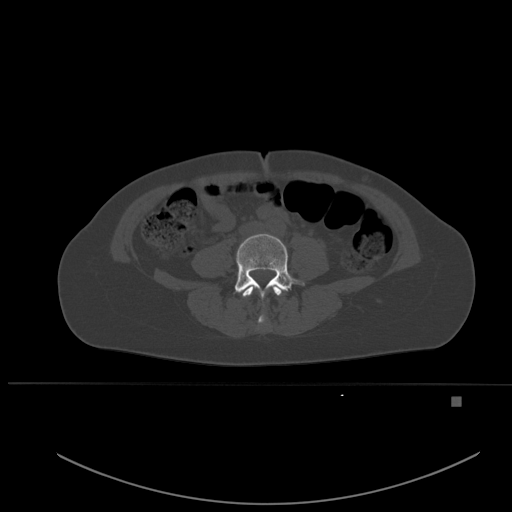
CT including the spine, one axial slice; slice 177 of 651 in the series (ordered by position); bone window (W 1800 / L 400 HU); 1.5 mm slice thickness; 512 × 512 image matrix, field of view 443 × 443 mm. Female patient, age 49 years. From the clinical record (not read from this slice): primary cancer: breast; vertebrae with lytic lesions (as recorded): L3, T12, L4.
Structures marked on this image (semi-automatically segmented with operator editing):
- L3 vertebra: bounding box (x1, y1, x2, y2) in pixels: (242, 285, 282, 323)
- L4 vertebra: (234, 234, 305, 298)